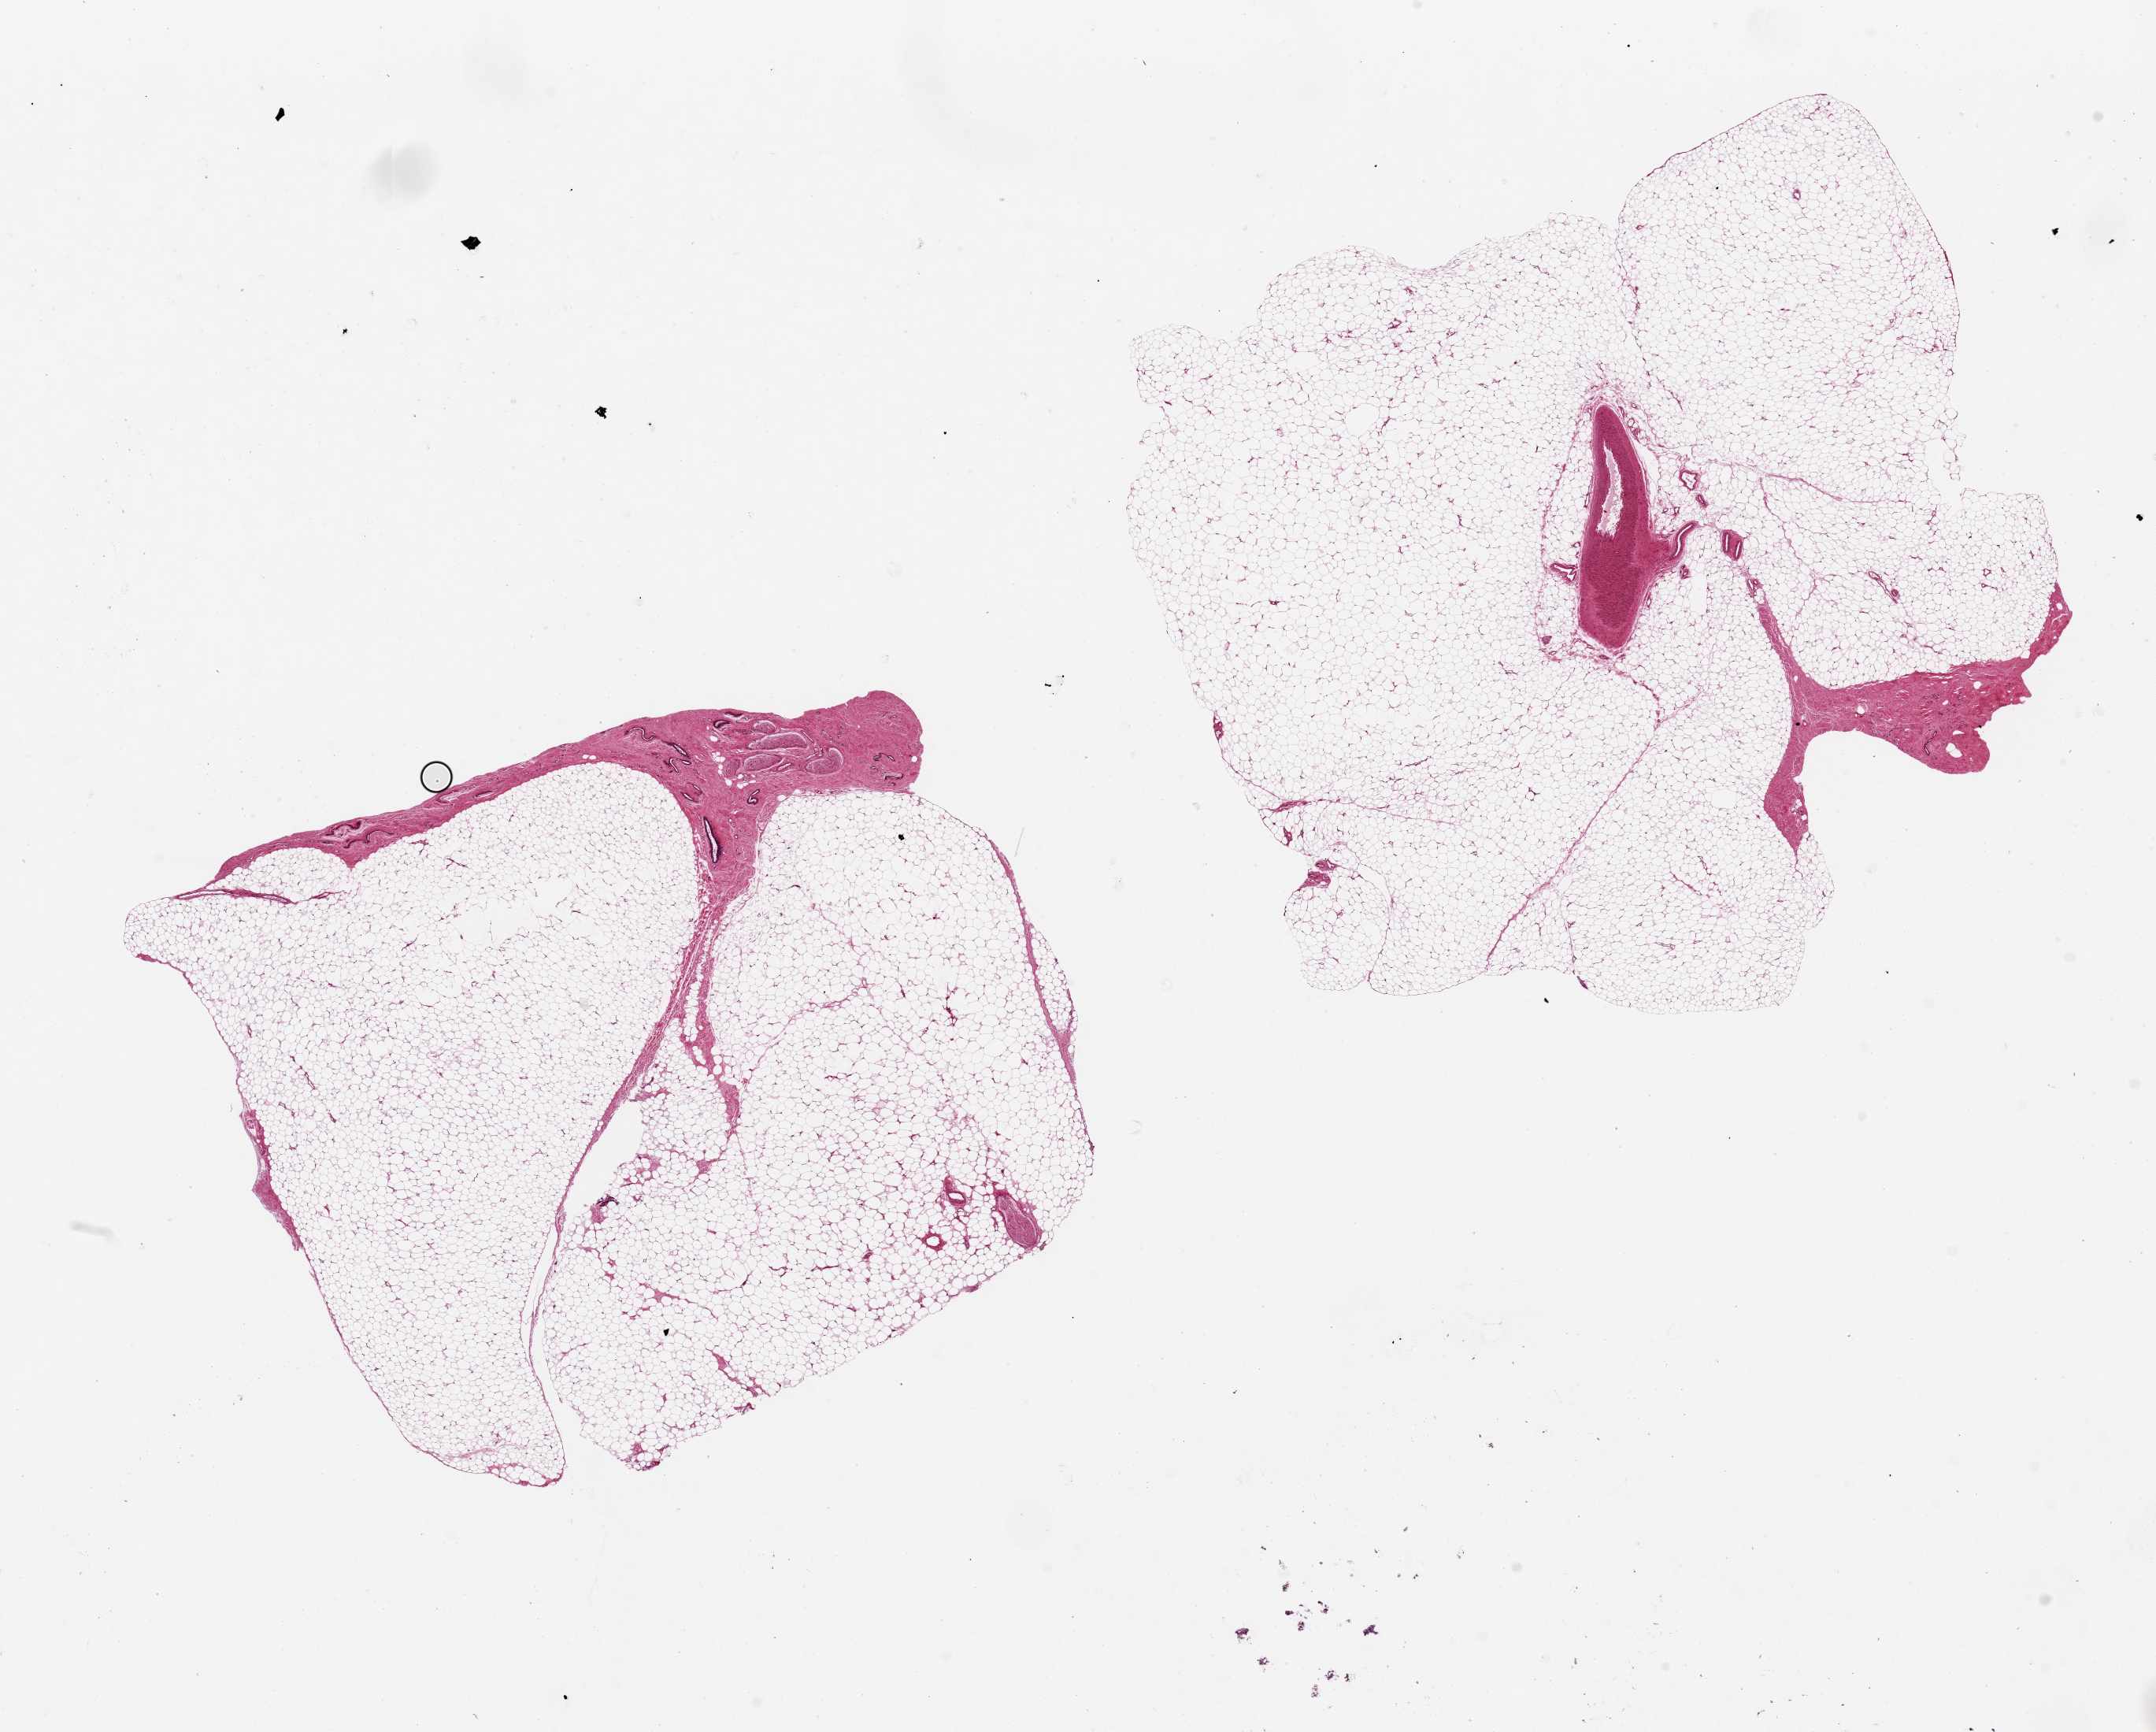
Digitized haematoxylin and eosin-stained section, brightfield, a low-resolution overview of the entire scanned area, about 21.7 x 17.4 mm (acquisition: 20x scan). PAXgene-fixed, paraffin-embedded tissue. Section of breast (target tissue). Tissue donor sample. Donor: male.
Review note (as recorded): 2 pieces, 10x9 & 10x10mm; larger has ducts in fibrous tissue; both 90% adipose.